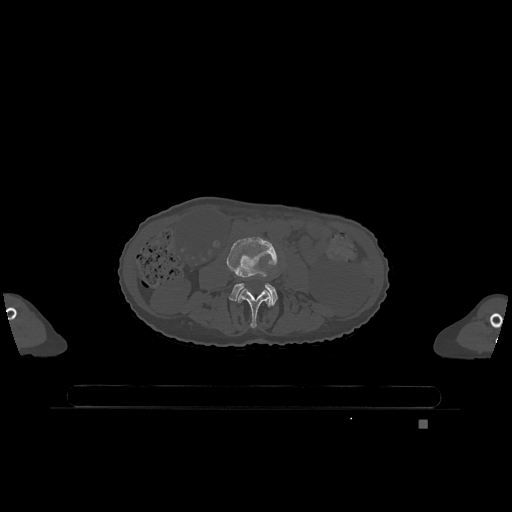
CT including the spine, one axial slice. Slice 331 of 1317 in the series (ordered by position). Bone window (W 1800 / L 400 HU). 0.5 mm slice thickness. 512 × 512 image matrix, field of view 500 × 500 mm. Female patient, age 74 years. Case-level facts recorded for this patient, not image findings: primary cancer: lung.
Annotated regions visible in this slice (semi-automatic segmentation, software-assisted and operator-edited):
- L3 vertebra: bounding box <238,288,271,328> (left, top, right, bottom; pixels)
- L4 vertebra: <227,237,278,305>